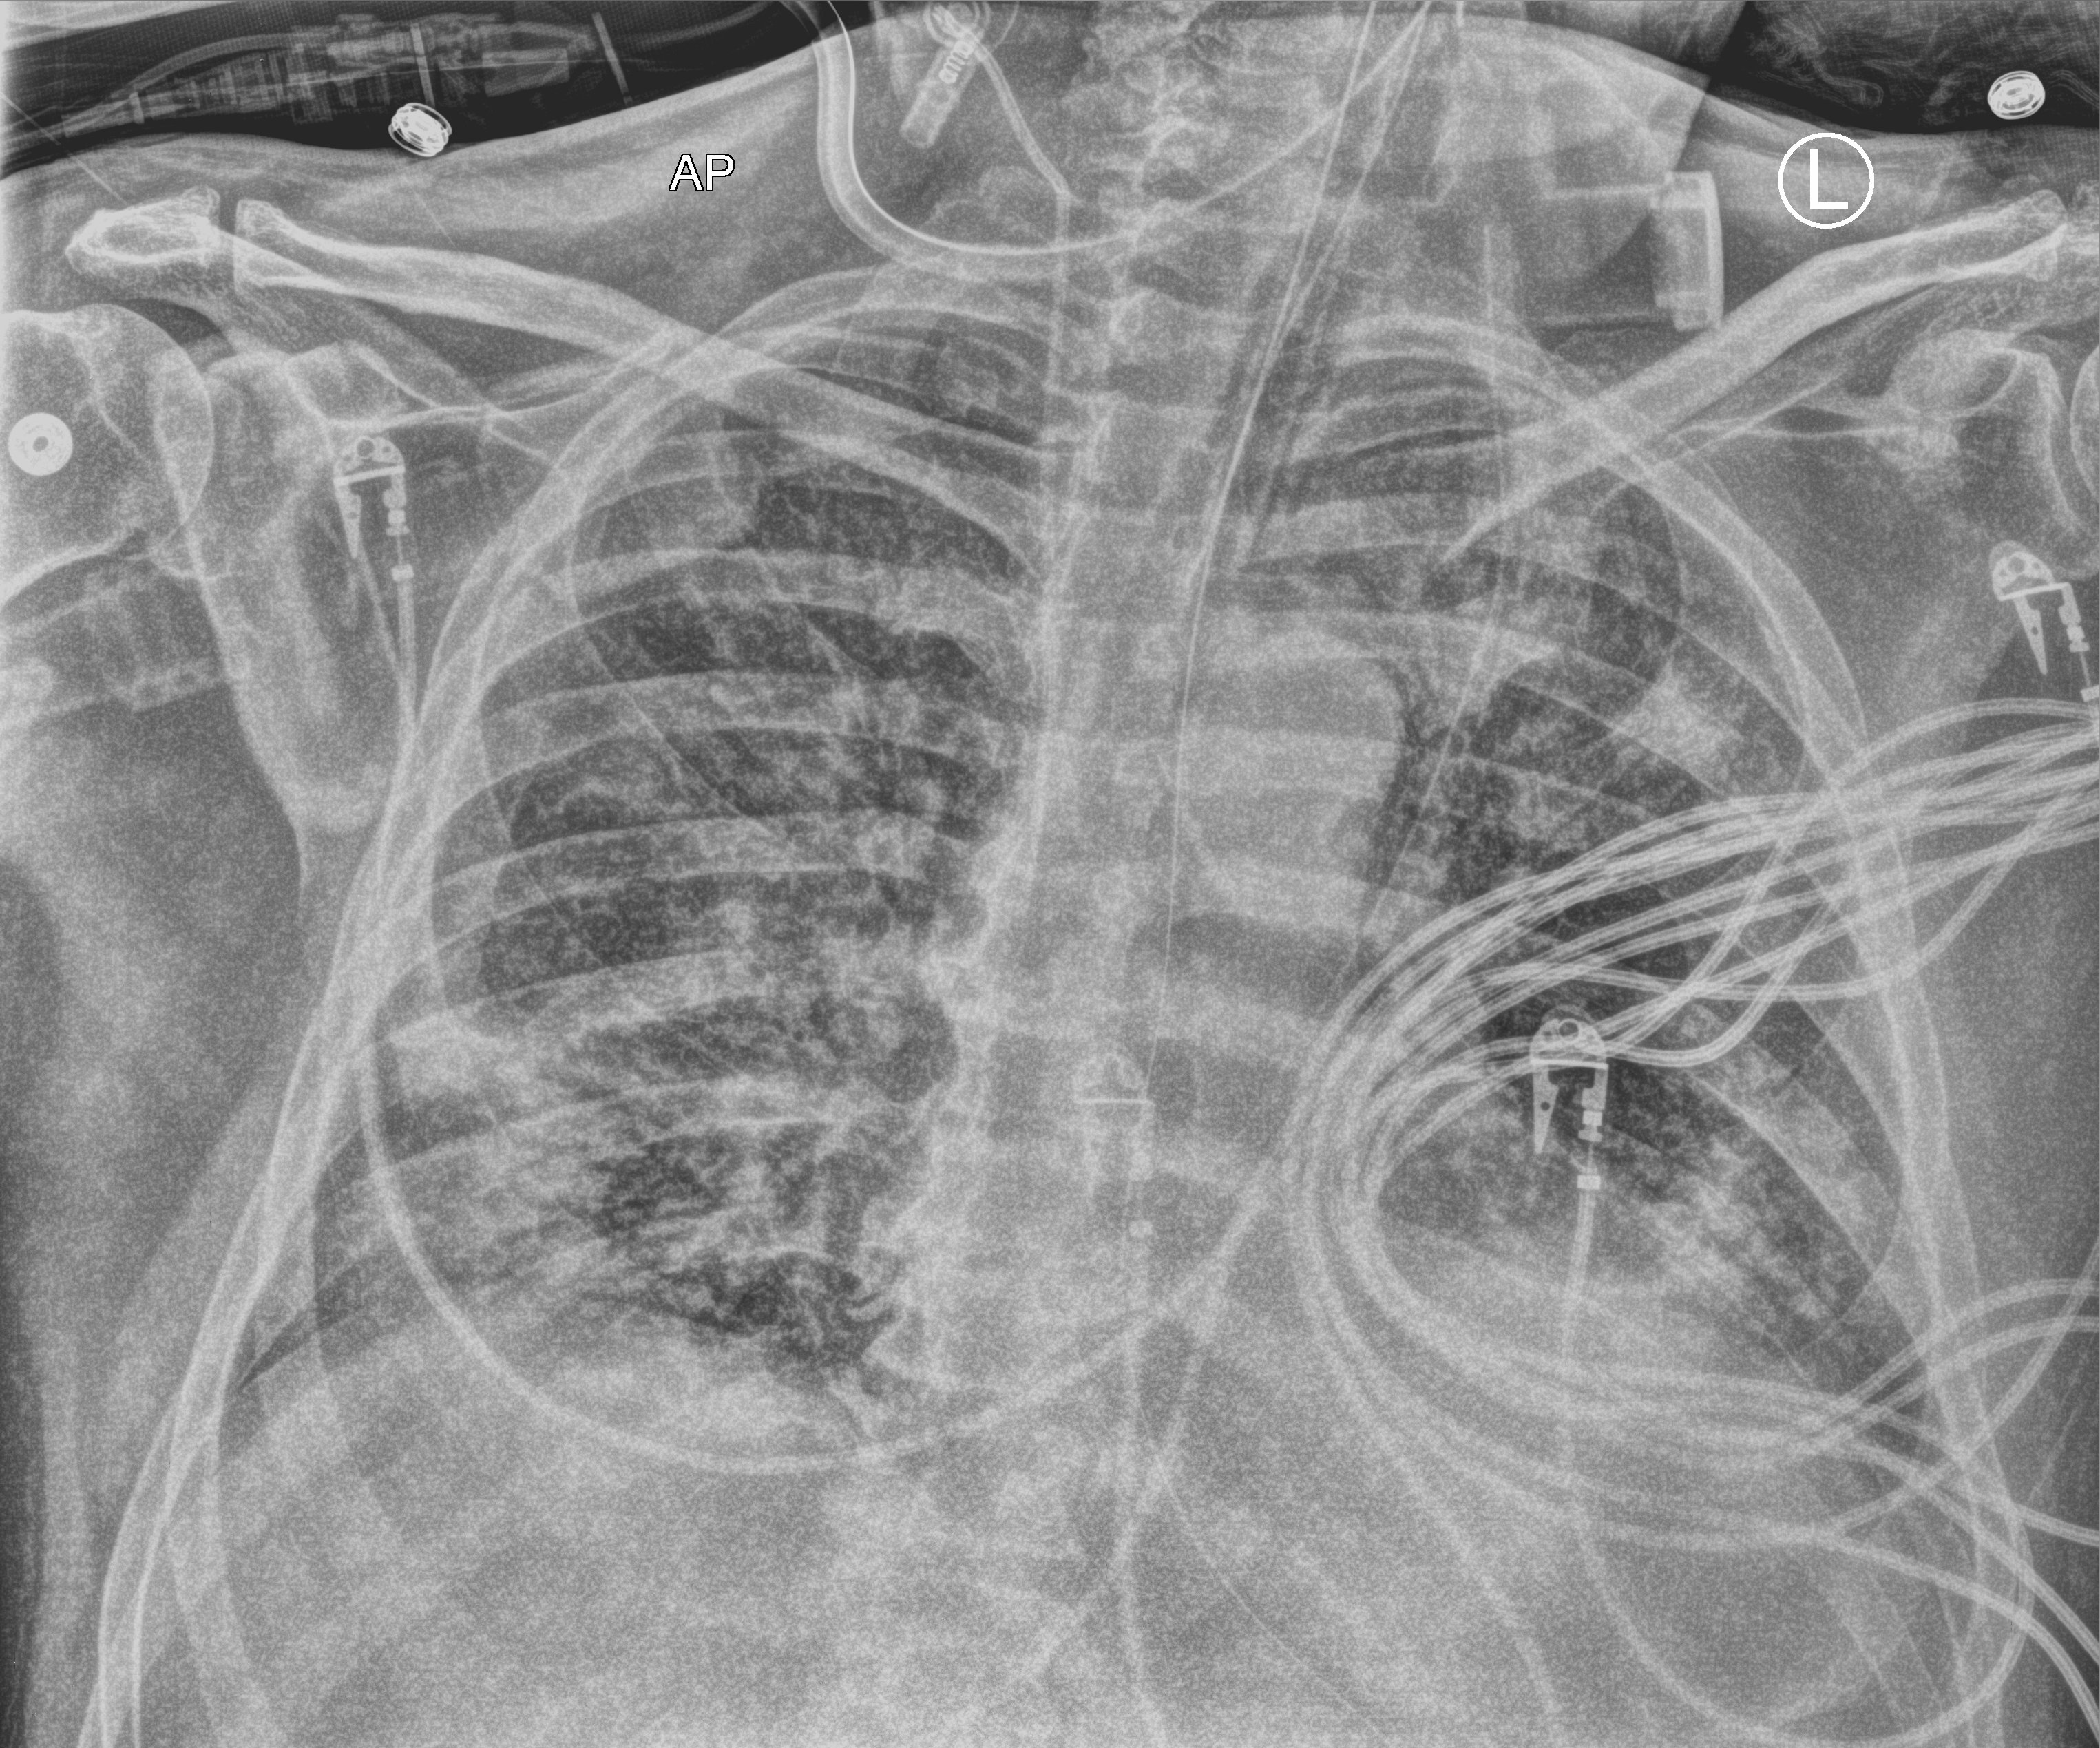
Chest X-ray (portable), anteroposterior (AP) projection. Male patient hospitalised with COVID-19, age 60–74 years.
Admission-level facts for this patient (not findings on this image; timing relative to this image not recorded): length of hospital stay: 33 days; mechanically ventilated during this hospital stay: yes; admitted to intensive care during this hospital stay: yes.